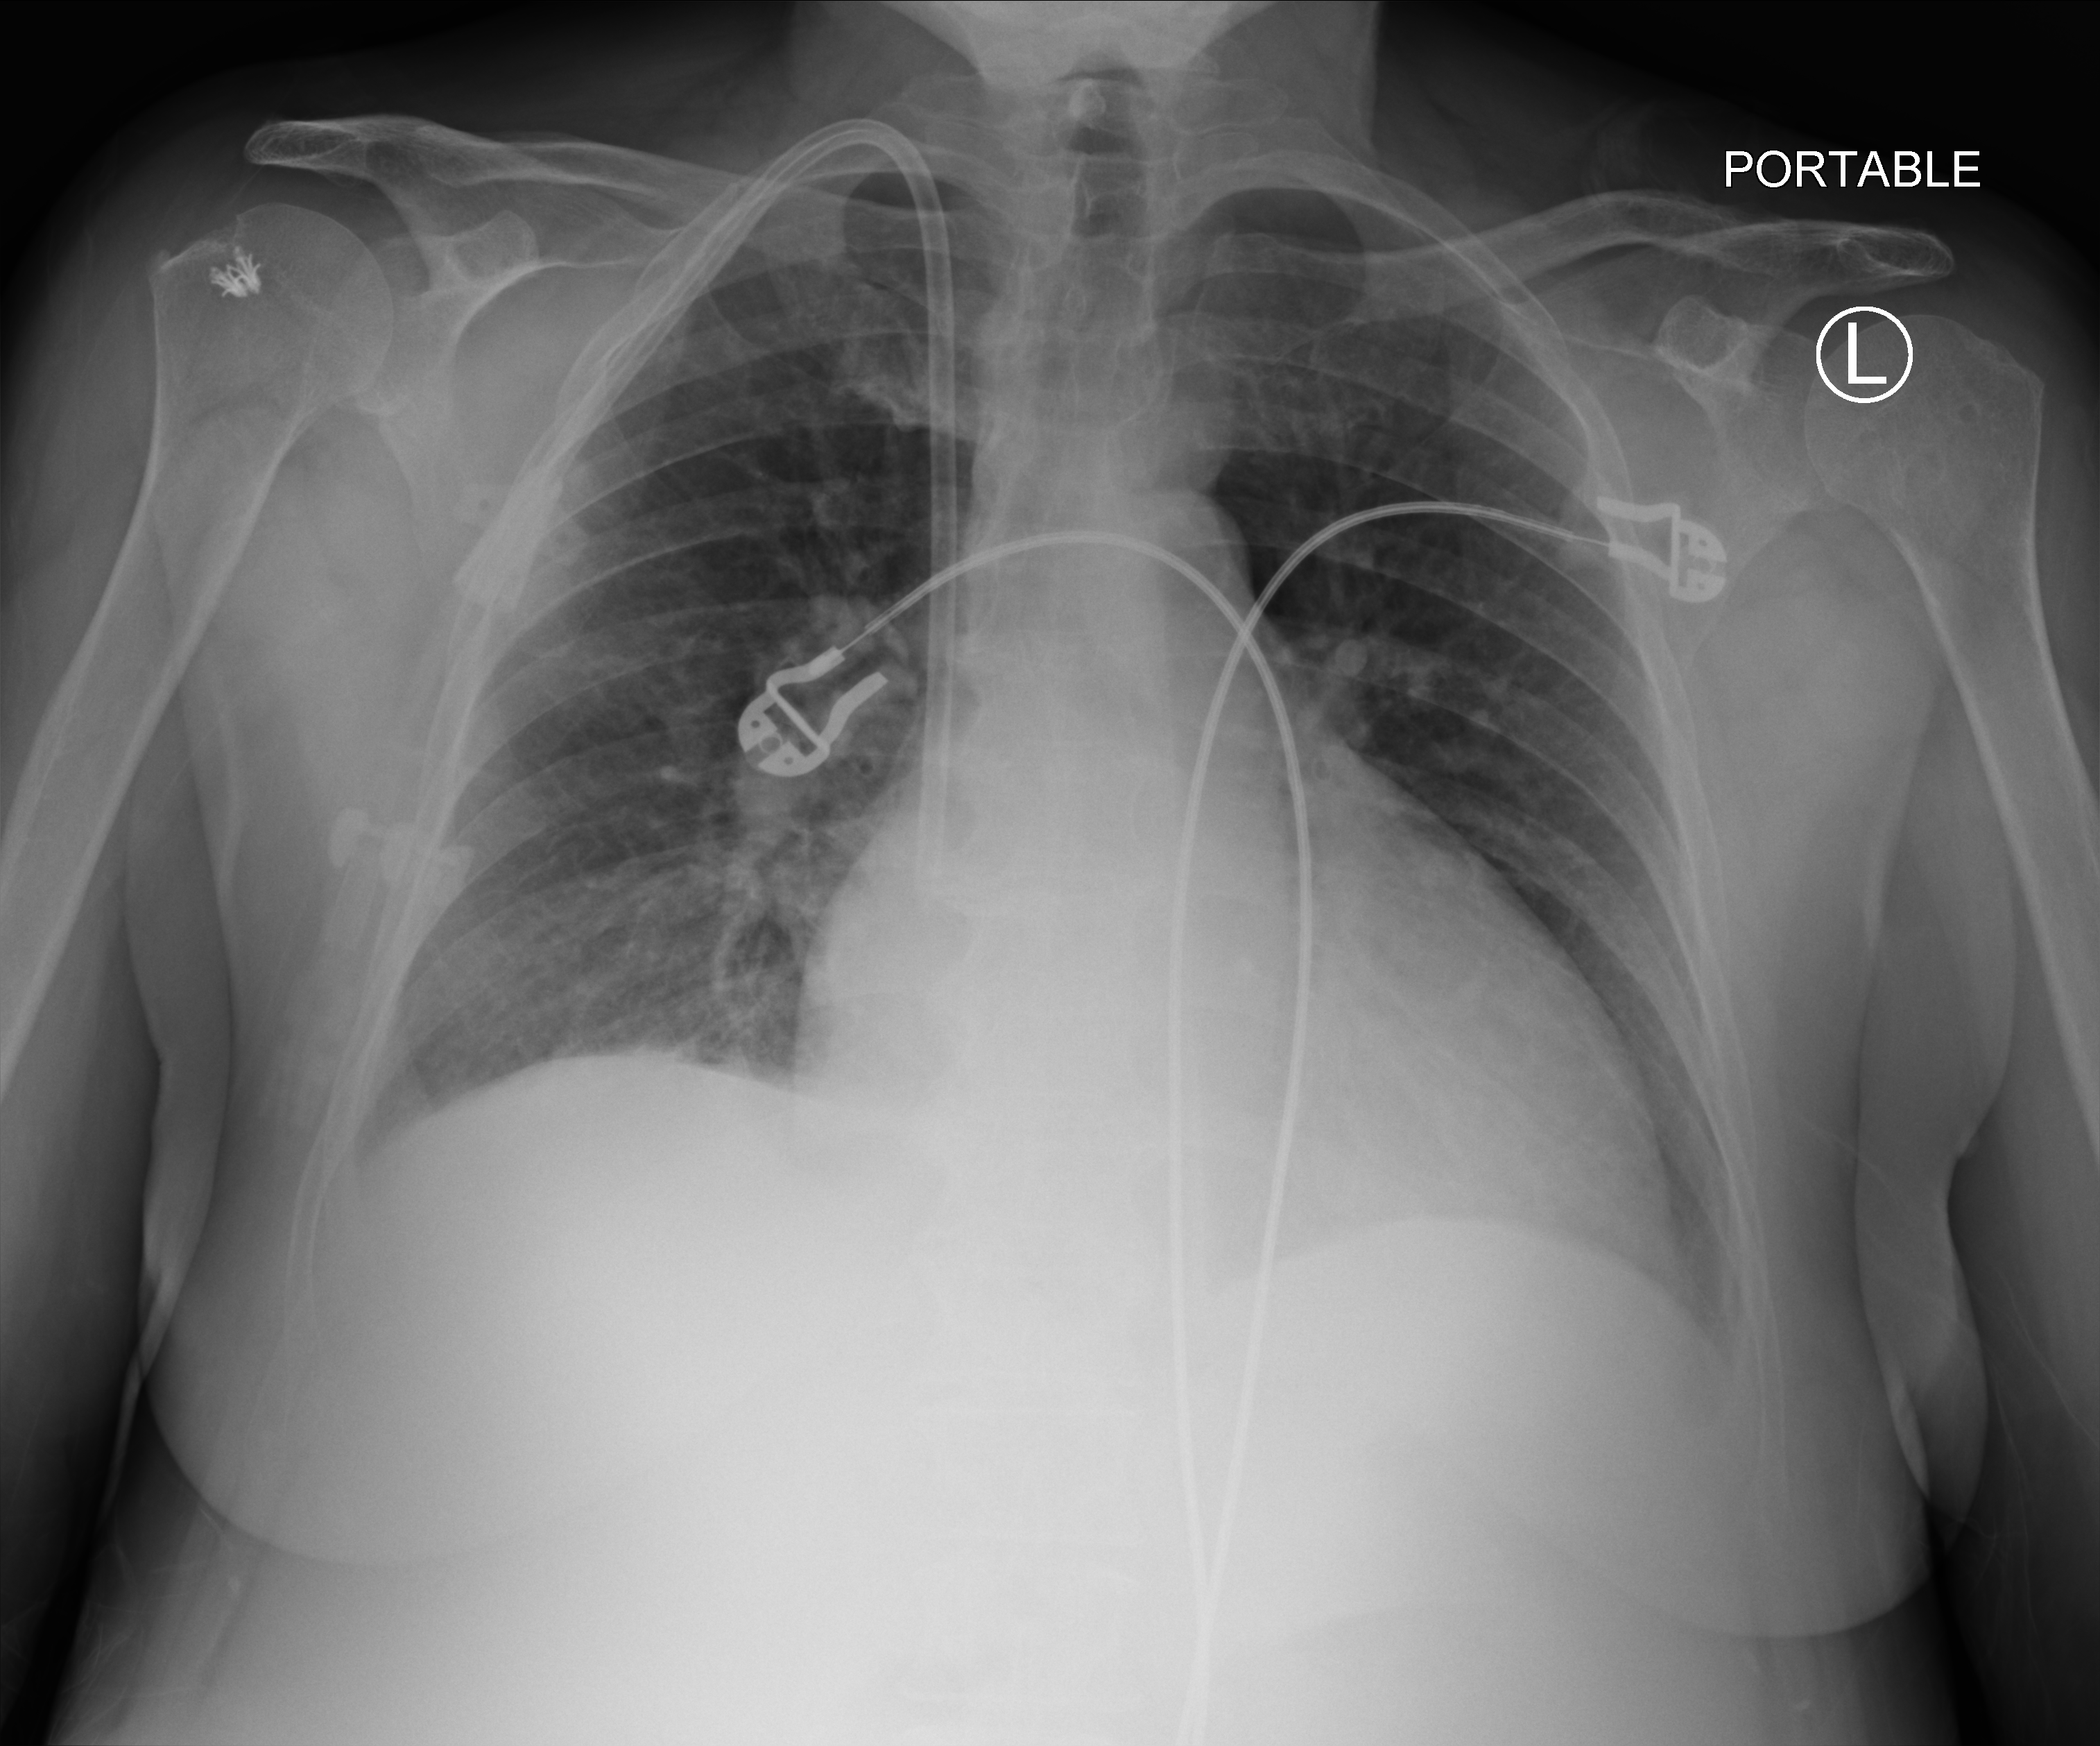
Chest X-ray (portable), anteroposterior (AP) projection. Patient hospitalised with COVID-19; female, aged 60–74 years.
Hospital-stay facts (about this admission, not read from this image; timing relative to this image not recorded):
- admitted to intensive care during this hospital stay: no